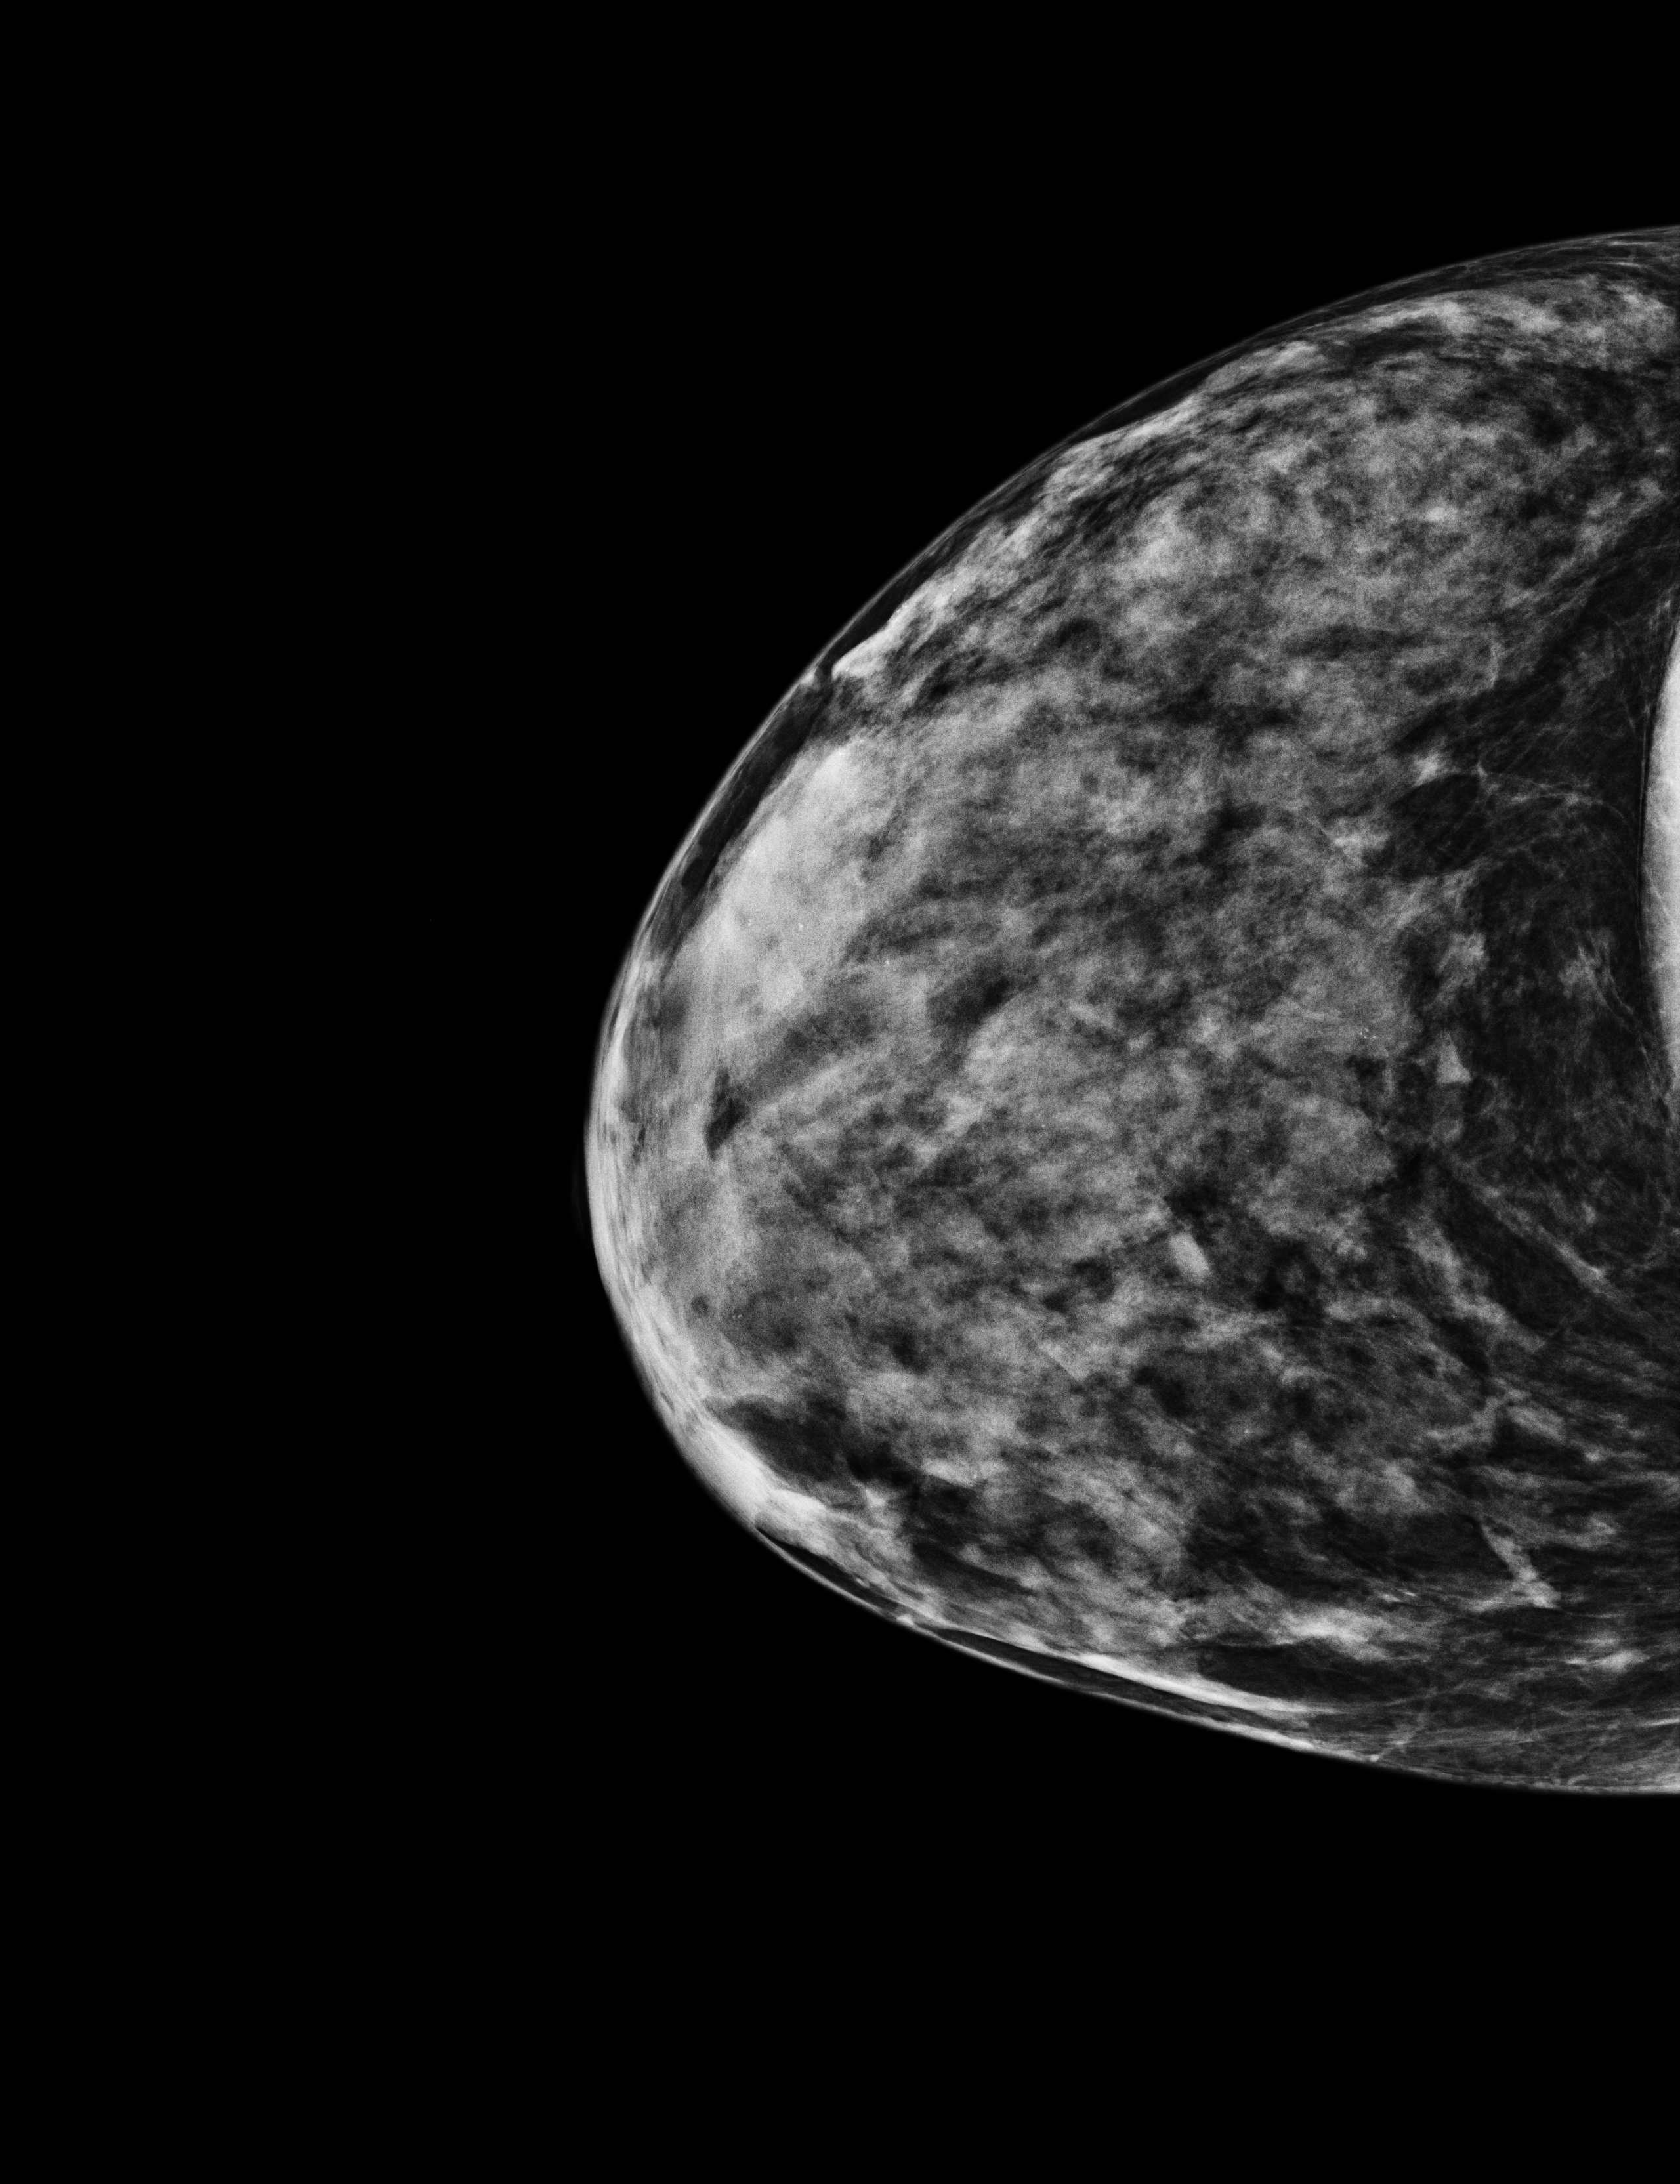
Digital mammogram (FFDM), right breast, craniocaudal (CC) view, annual screening mammography examination, compressed breast thickness 37 mm. Patient: female, 43 years.
Breast density at the screening exam (both breasts): extremely dense (BI-RADS density category d). Final BI-RADS category for the screening round (tomosynthesis exam, both breasts): category 2. Recall: no recall after this screen.